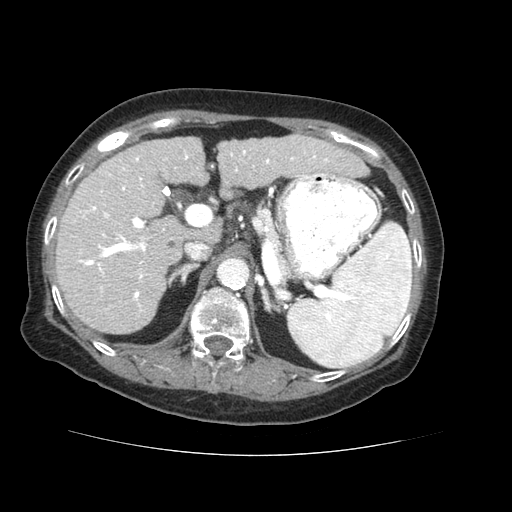
Contrast-enhanced abdominal CT (liver protocol), one axial slice; reconstruction kernel STANDARD; soft-tissue window (W 400 / L 40 HU); 2.5 mm slice thickness; 512 × 512 image matrix. From the clinical record (not read from this slice): diagnosis: hepatocellular carcinoma (patient treated with transarterial chemoembolisation; whether this scan precedes or follows treatment is not stated here); TNM stage (as recorded): Stage-IVB; Child-Pugh class: A.
Annotated regions visible in this slice (semi-automatically segmented with operator editing):
- liver parenchyma outside the tumour (the mass and vessels are separate outlines, so this box may not span the whole liver): bounding box (x1, y1, x2, y2) in pixels: (56, 134, 368, 334)
- liver vessels: (79, 150, 329, 312)